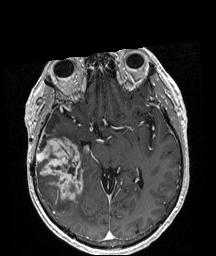
Brain MRI from a brain-tumour surgery series, one axial slice. Slice 114 of 208 in the series (ordered by position). T1-weighted post-contrast. 216 × 256 image matrix, field of view 211 × 250 mm. Case-level facts recorded for this patient, not image findings: histopathology: Astrocytoma; WHO grade: 4; IDH mutation: yes.
Annotated regions visible in this slice (manually delineated by an expert):
- tumour: bounding box (x1, y1, x2, y2) in pixels: (36, 138, 83, 200)